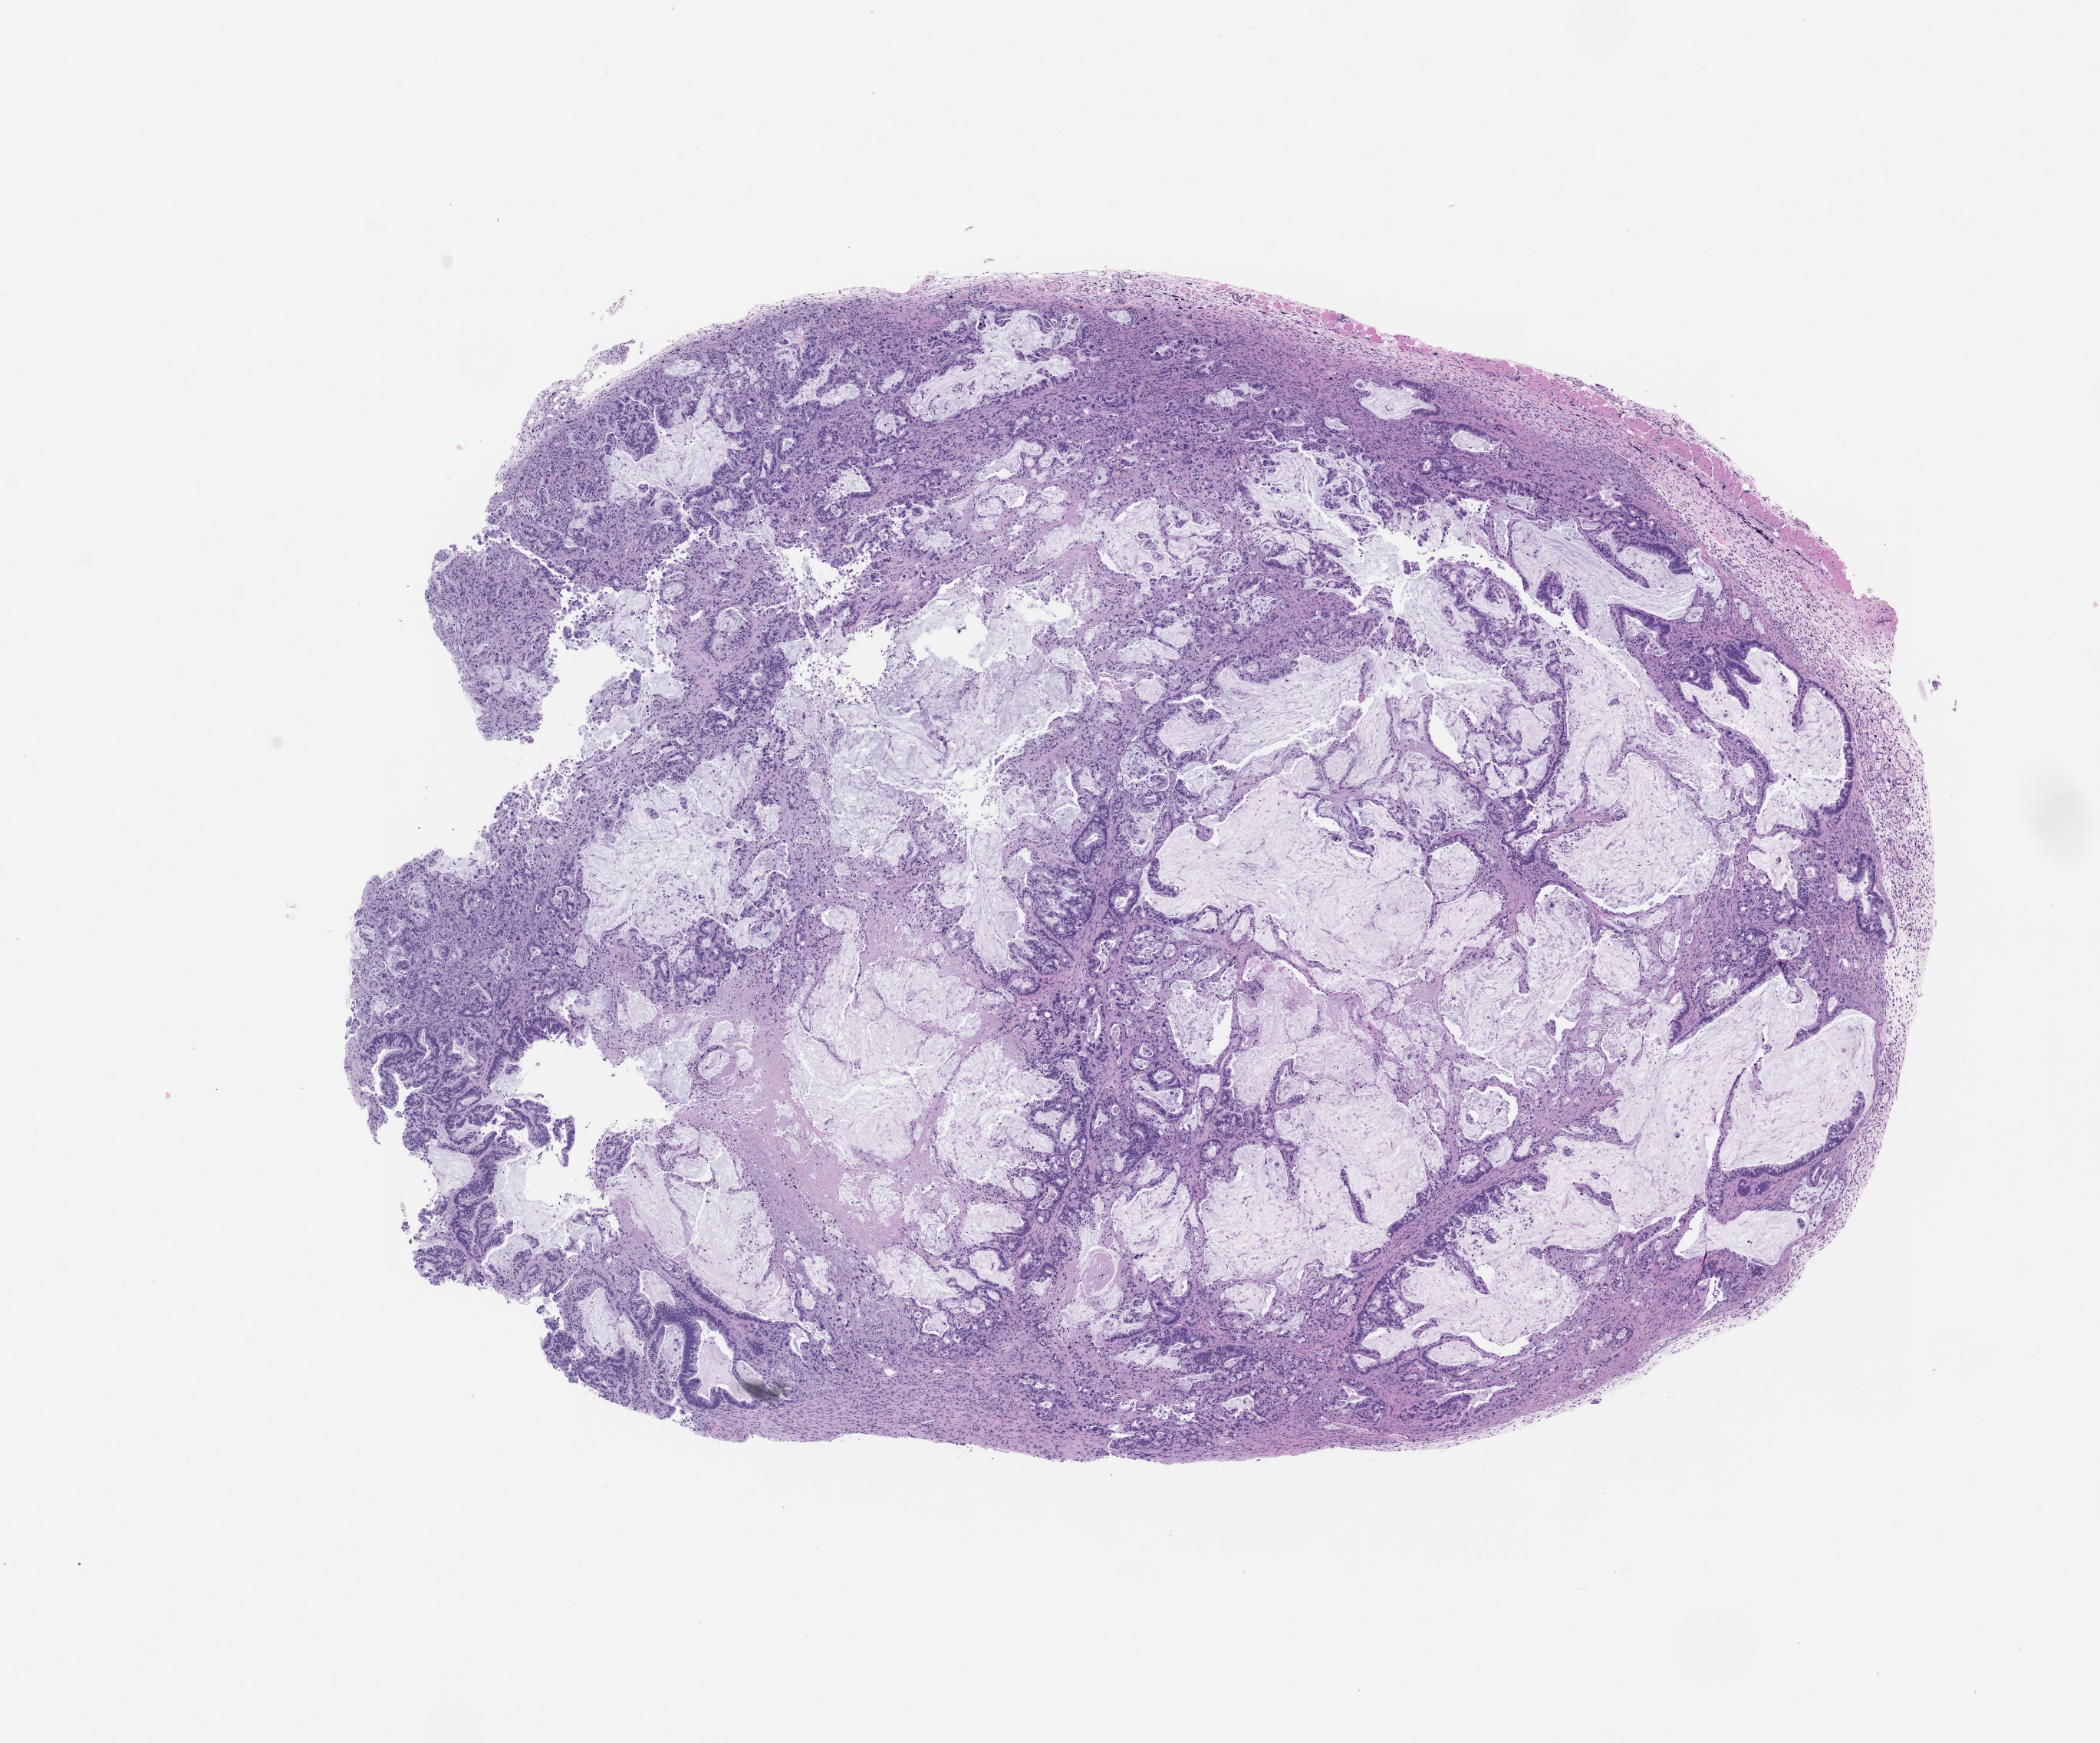
Hematoxylin and eosin (H&E) whole-slide image of a patient-derived xenograft (PDX) tumor grown in a mouse, passage 0 — whole scanned area (about 11.0 x 9.1 mm) shown as a low-resolution overview. FFPE section. Originating tumor site category: pancreas.
Originating patient diagnosis: Pancreatic Adenocarcinoma.